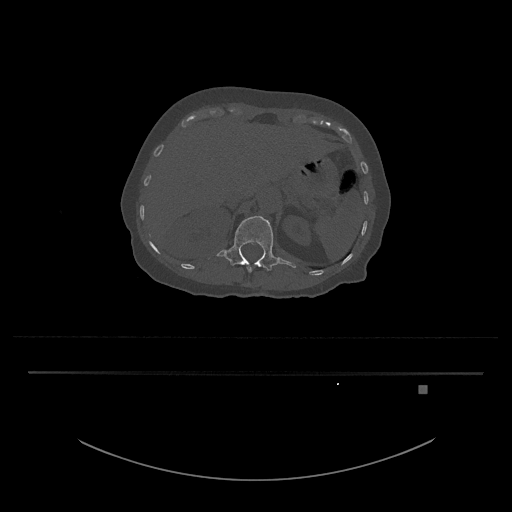
CT including the spine, one axial slice. Position 558 of 797 along the scan axis. 120 kVp. Bone window (W 1800 / L 400 HU). 0.5 mm slice thickness. 512 × 512 image matrix, field of view 500 × 500 mm. Patient: female, 57 years. Case-level facts recorded for this patient, not image findings: primary cancer: cervical.
Structures marked on this image (semi-automatic segmentation, software-assisted and operator-edited):
- L1 vertebra: bounding box <208,216,296,273> (left, top, right, bottom; pixels)